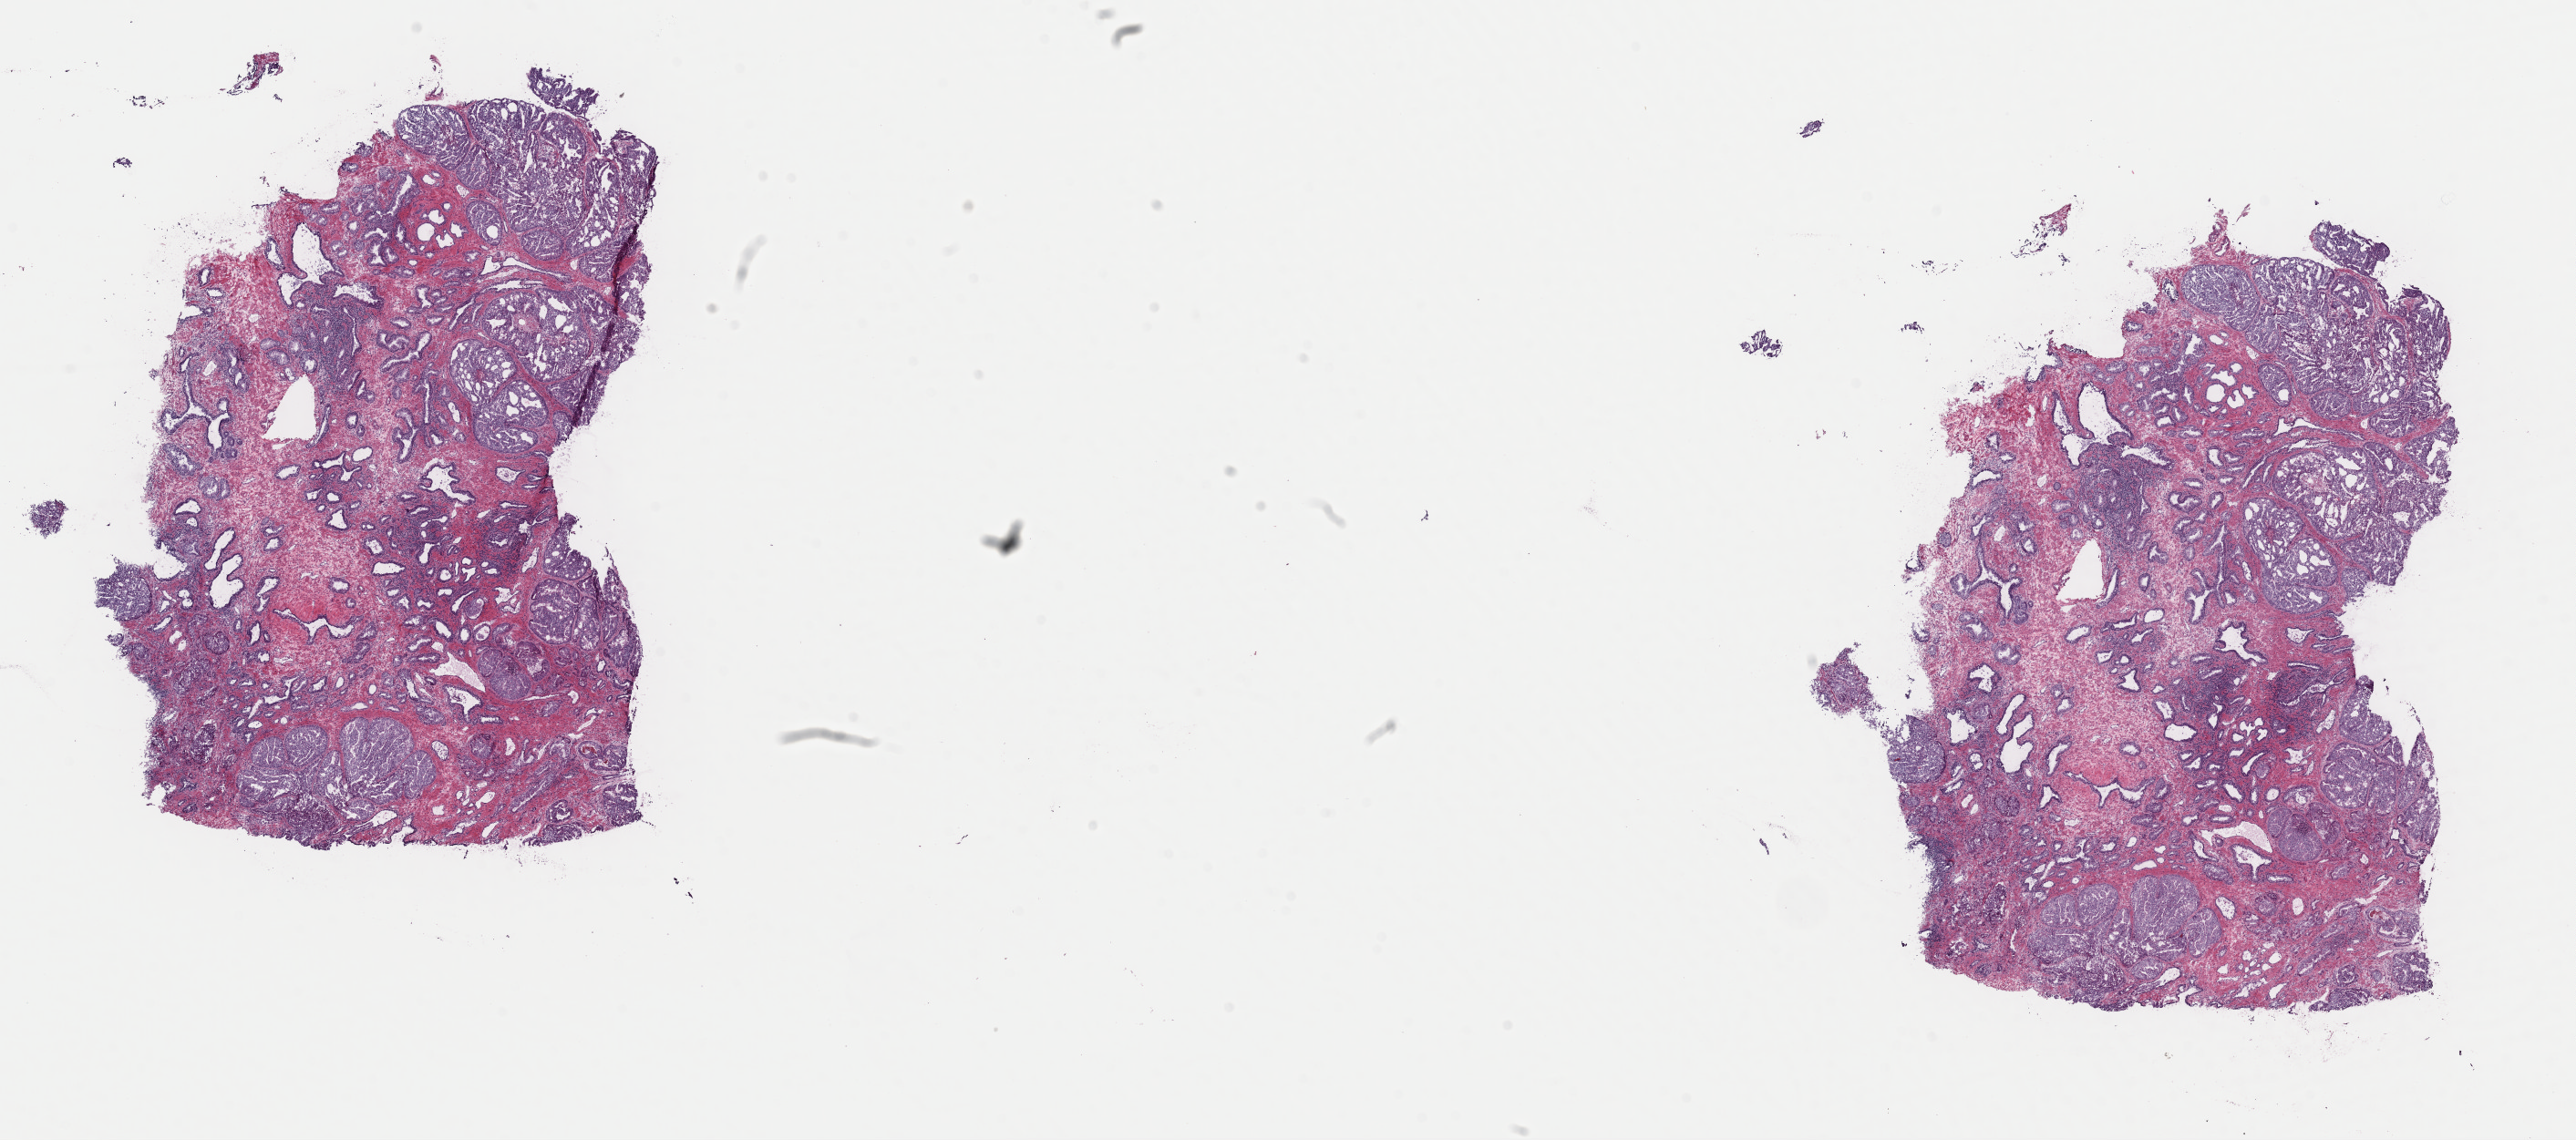
H&E whole-slide image — a low-resolution overview of the entire scanned area, about 22.3 x 9.9 mm (from a 40x scan), frozen section from the top of the tissue portion, sample: primary tumour, prostate. Male patient; age at initial diagnosis 57 years. Composition of this section per pathologist review: tumour cells 45%, tumour nuclei 60%.
Histologic diagnosis: Adenocarcinoma, NOS (prostate gland).